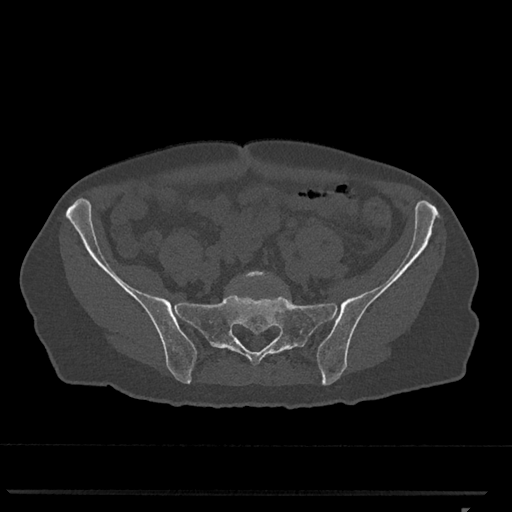
CT including the spine, one axial slice; 120 kVp; bone window (W 1800 / L 400 HU); 0.5 mm slice thickness; 512 × 512 image matrix, field of view 380 × 380 mm. Patient: female, 62 years. From the clinical record (not read from this slice): primary cancer: renal.
Structures marked on this image (semi-automatic segmentation, software-assisted and operator-edited):
- L5 vertebra: box from (x=240, y=271) to (x=271, y=280) px